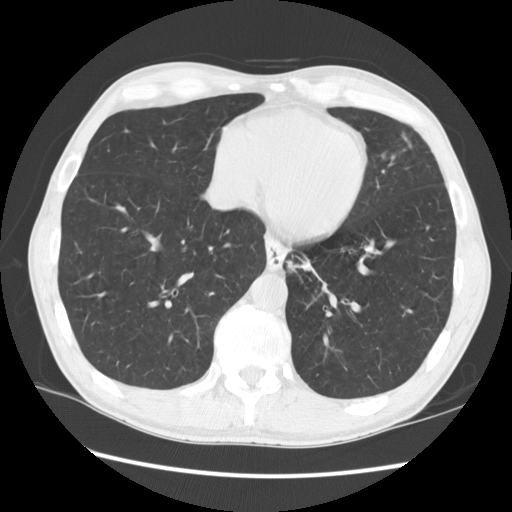
Axial slice from a low-dose chest CT screening exam; baseline annual screen; lung window (W 1500 / L -600 HU). Male, age 57 years at enrolment. Current smoker at enrolment.
Expert reader's lesion annotation, bounding box <269,241,337,303> (left, top, right, bottom; pixels). The screening reader recorded 2 non-calcified nodules or masses ≥4 mm on this exam (left lower lobe, lingula); which of them this box marks is not recorded. Official screen result: positive, change unspecified: nodule(s) >= 4 mm or enlarging nodule(s), mass(es), or other non-specific abnormalities suspicious for lung cancer. Participant outcome: lung cancer diagnosed 95 days after this screen — squamous cell carcinoma, NOS, left lower lobe, moderately differentiated (G2), stage IB (AJCC 6th edition), 35 mm at pathology.